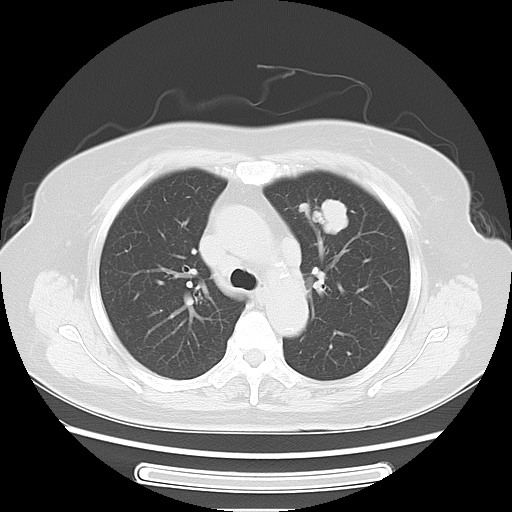
Chest CT, one axial slice; slice 42 of 57 in the series (ordered by position); reconstruction kernel LUNG; 120 kVp; lung window (W 1500 / L -600 HU); 5 mm slice thickness; 512 × 512 image matrix. Female patient, age 77 years. Case-level facts recorded for this patient, not image findings: clinical TNM (as recorded): T1c N3 M0.
Structures marked on this image (bounding box drawn by a radiologist):
- lung tumour (recorded histology: adenocarcinoma): bounding box <301,195,361,244> (left, top, right, bottom; pixels)